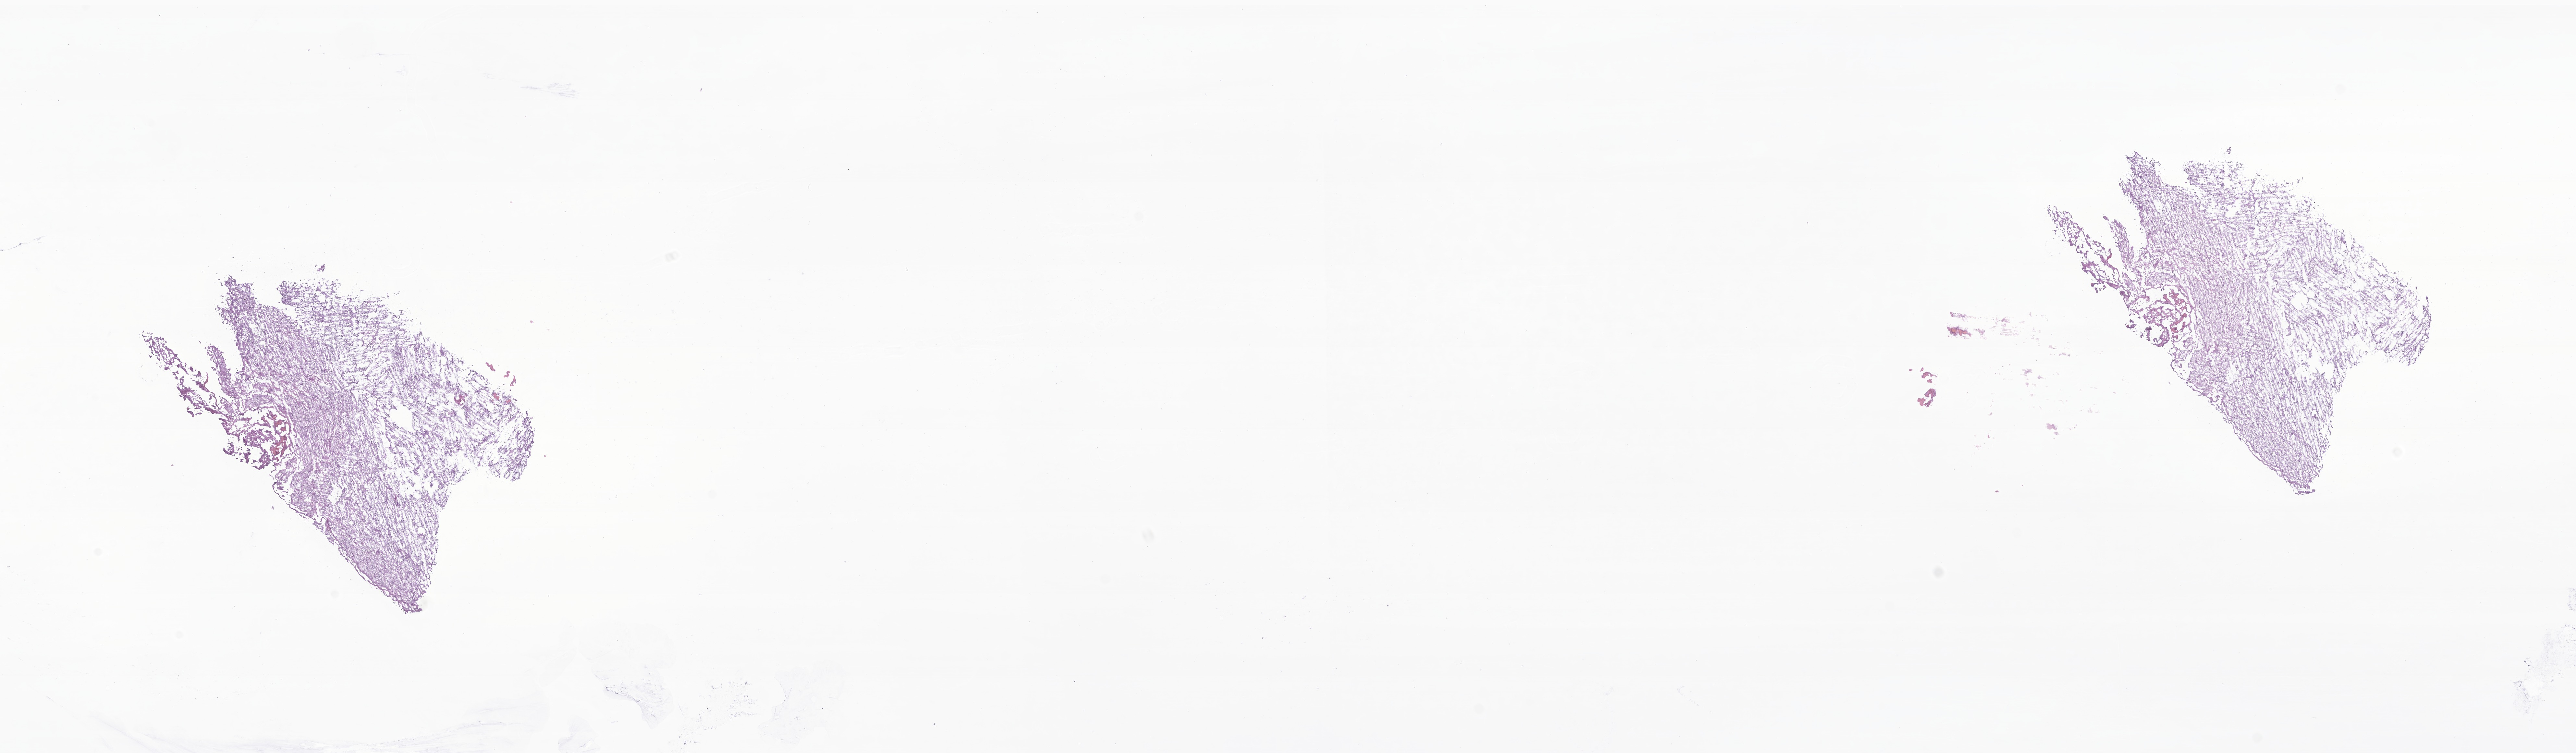
Whole-slide image, H&E stain of tumor tissue from the brain, low-resolution overview of the scanned area, about 33.5 x 9.8 mm, frozen section. Patient female; age 227 months (18 years 11 months).
Diagnosis: Pilocytic astrocytoma.